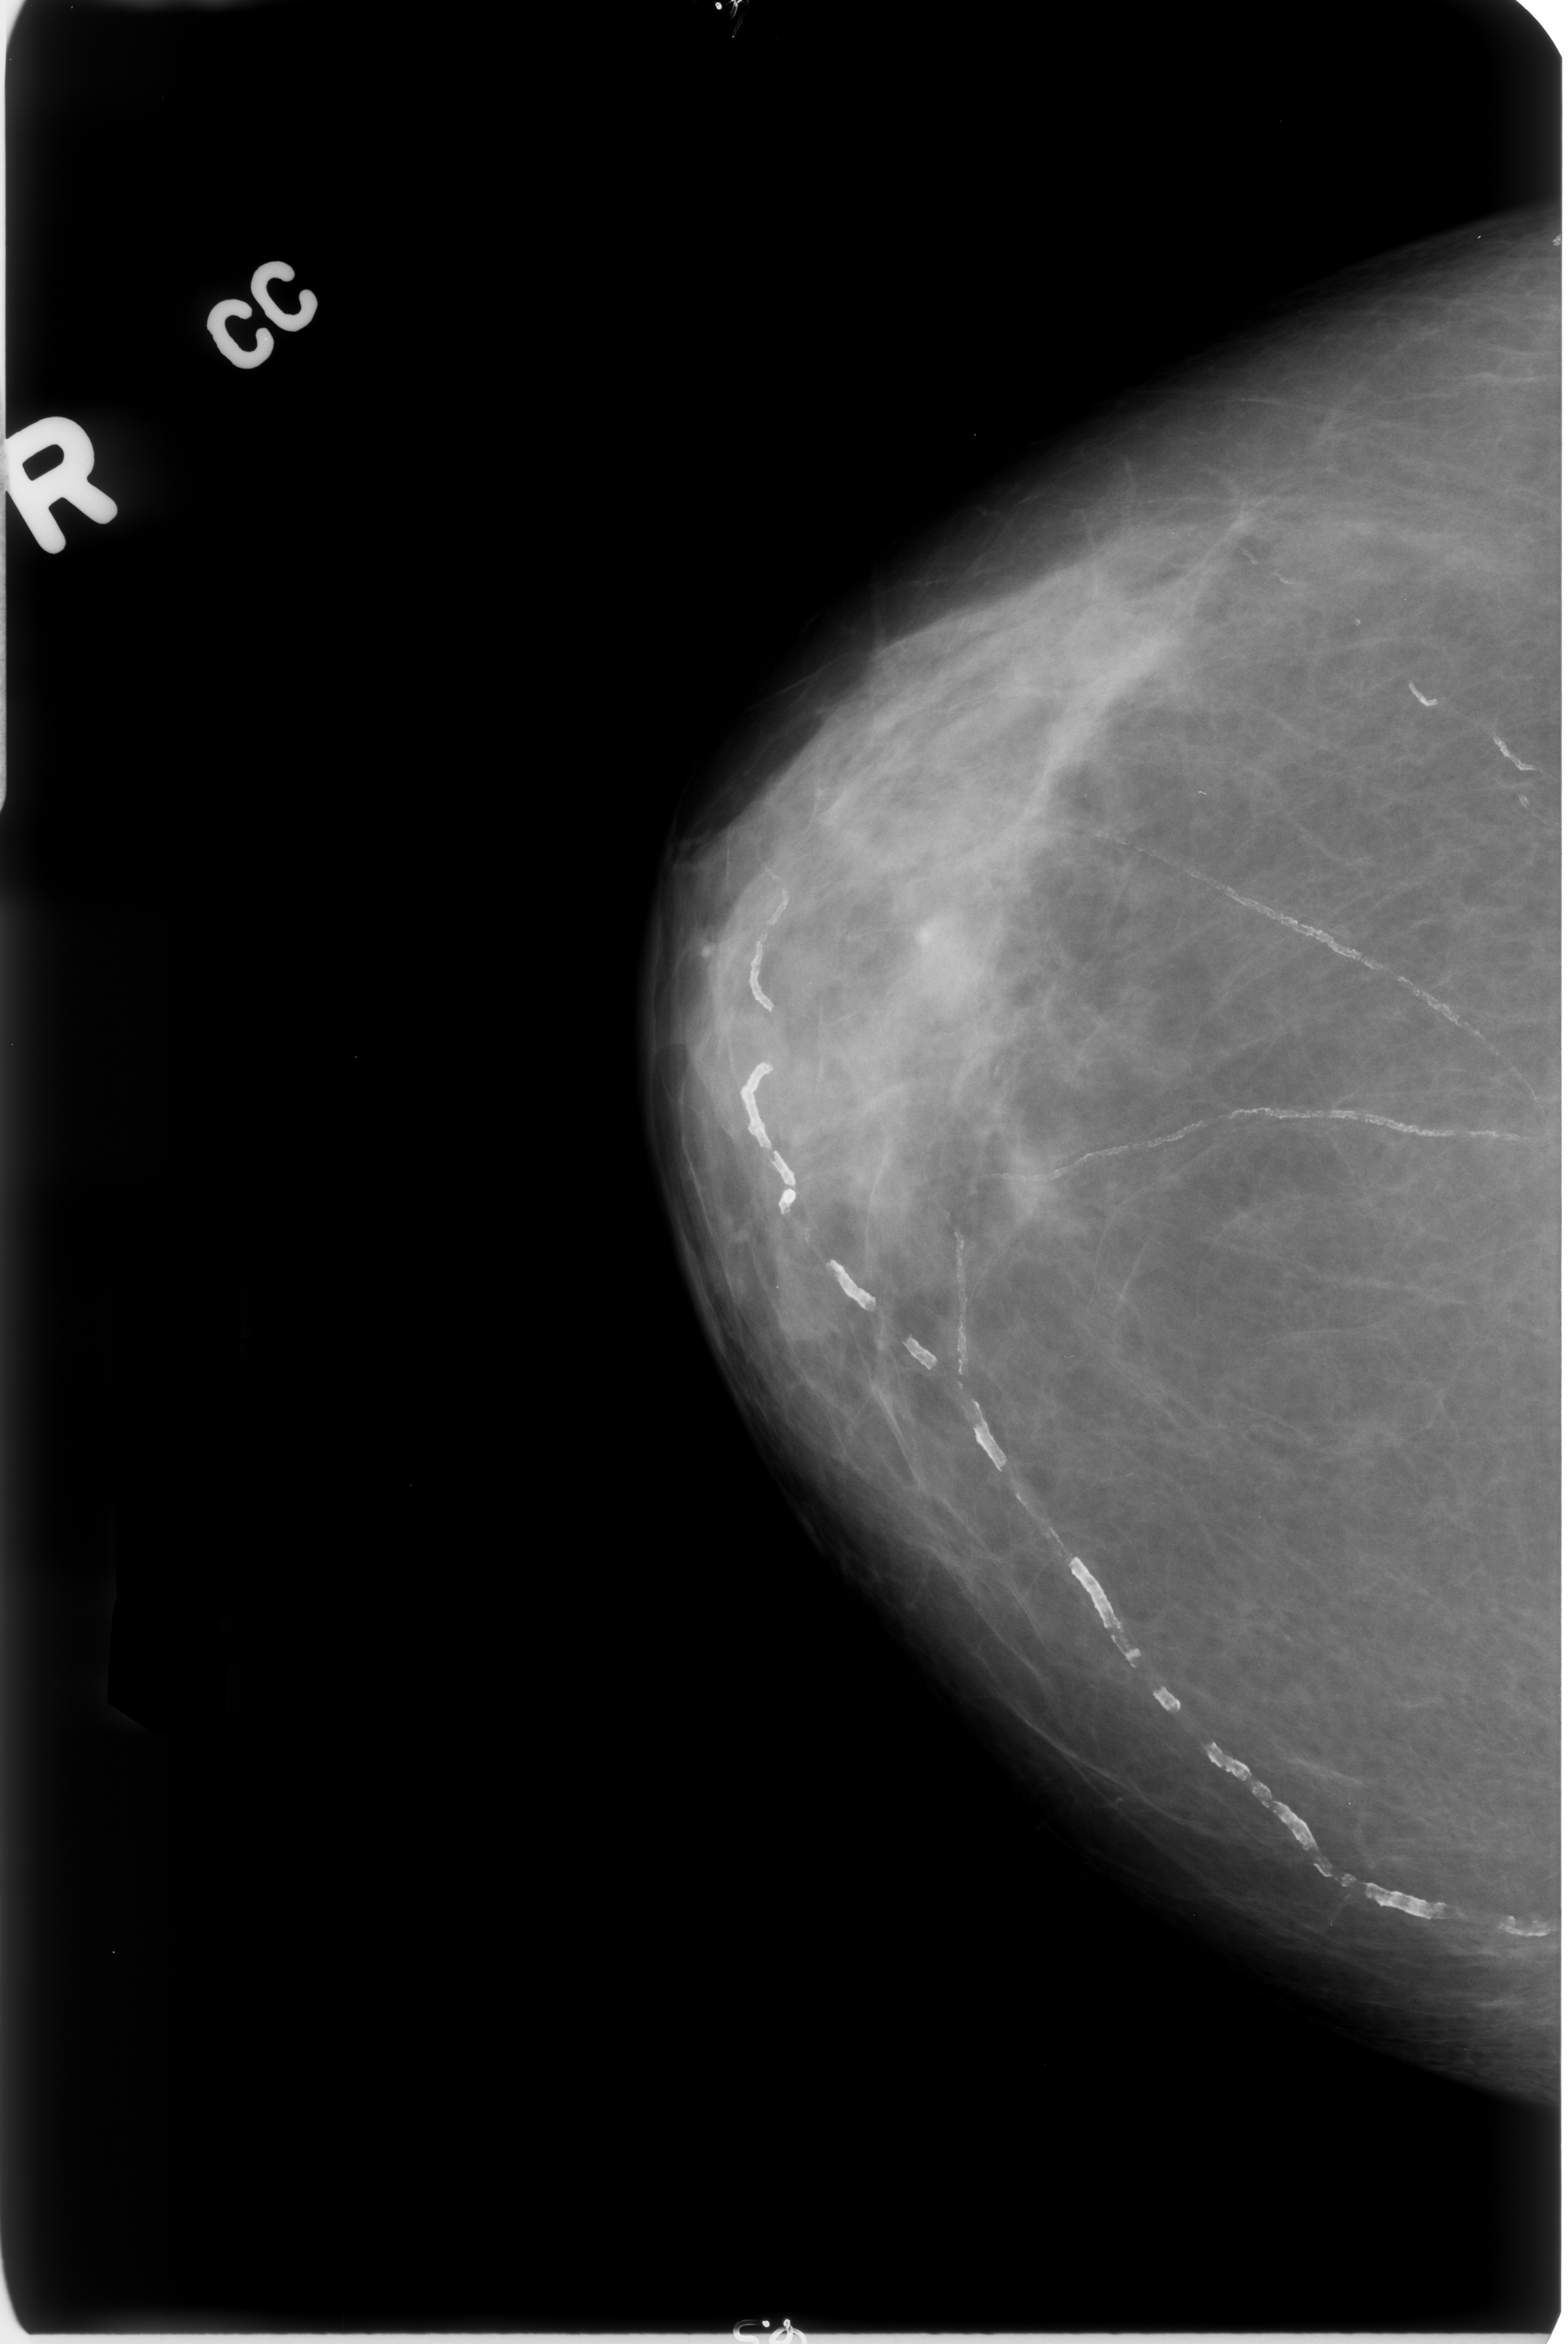
Scanned film-screen mammogram; right breast; CC view; breast composition: scattered fibroglandular densities (BI-RADS density category 2 of 4); 1568 × 2344 image matrix.
Expert-marked regions of interest on this image (one box per marked abnormality):
- Finding 1 of 3: calcifications, morphology vascular; BI-RADS assessment category 2; benign; no additional work-up was recommended (outcome (as recorded, no biopsy): benign without callback): bounding box <727,933,1557,1953> (left, top, right, bottom; pixels)
- Finding 2 of 3: calcifications, morphology vascular; BI-RADS assessment category 2; benign; no additional work-up was recommended (outcome (as recorded, no biopsy): benign without callback): <1042,1103,1516,1193>
- Finding 3 of 3: calcifications, morphology vascular; BI-RADS assessment category 2; subtlety rating 5 on a 1 (subtle) to 5 (obvious) scale; benign; no additional work-up was recommended (outcome (as recorded, no biopsy): benign without callback): <1171,852,1521,1092>